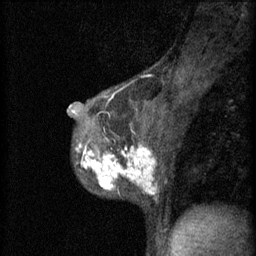
Breast MRI (dynamic contrast-enhanced), one sagittal slice; slice 37 of 60 in the series (ordered by position); 3 images stored at this slice position (order not interpretable as contrast timing); 1.5 T; TE 4.2 ms, TR 11 ms; 2 mm slice thickness; 256 × 256 image matrix. Female patient, age 37 years.
Outlined on this slice (semi-automatically segmented with operator editing):
- analysis volume of interest (the breast-tissue region the enhancement analysis was run in; not a lesion): bounding box (x1, y1, x2, y2) in pixels: (75, 138, 164, 195)
- tumour enhancement mask (voxels above the 70 % enhancement threshold inside the analysis volume of interest): (76, 142, 156, 195)